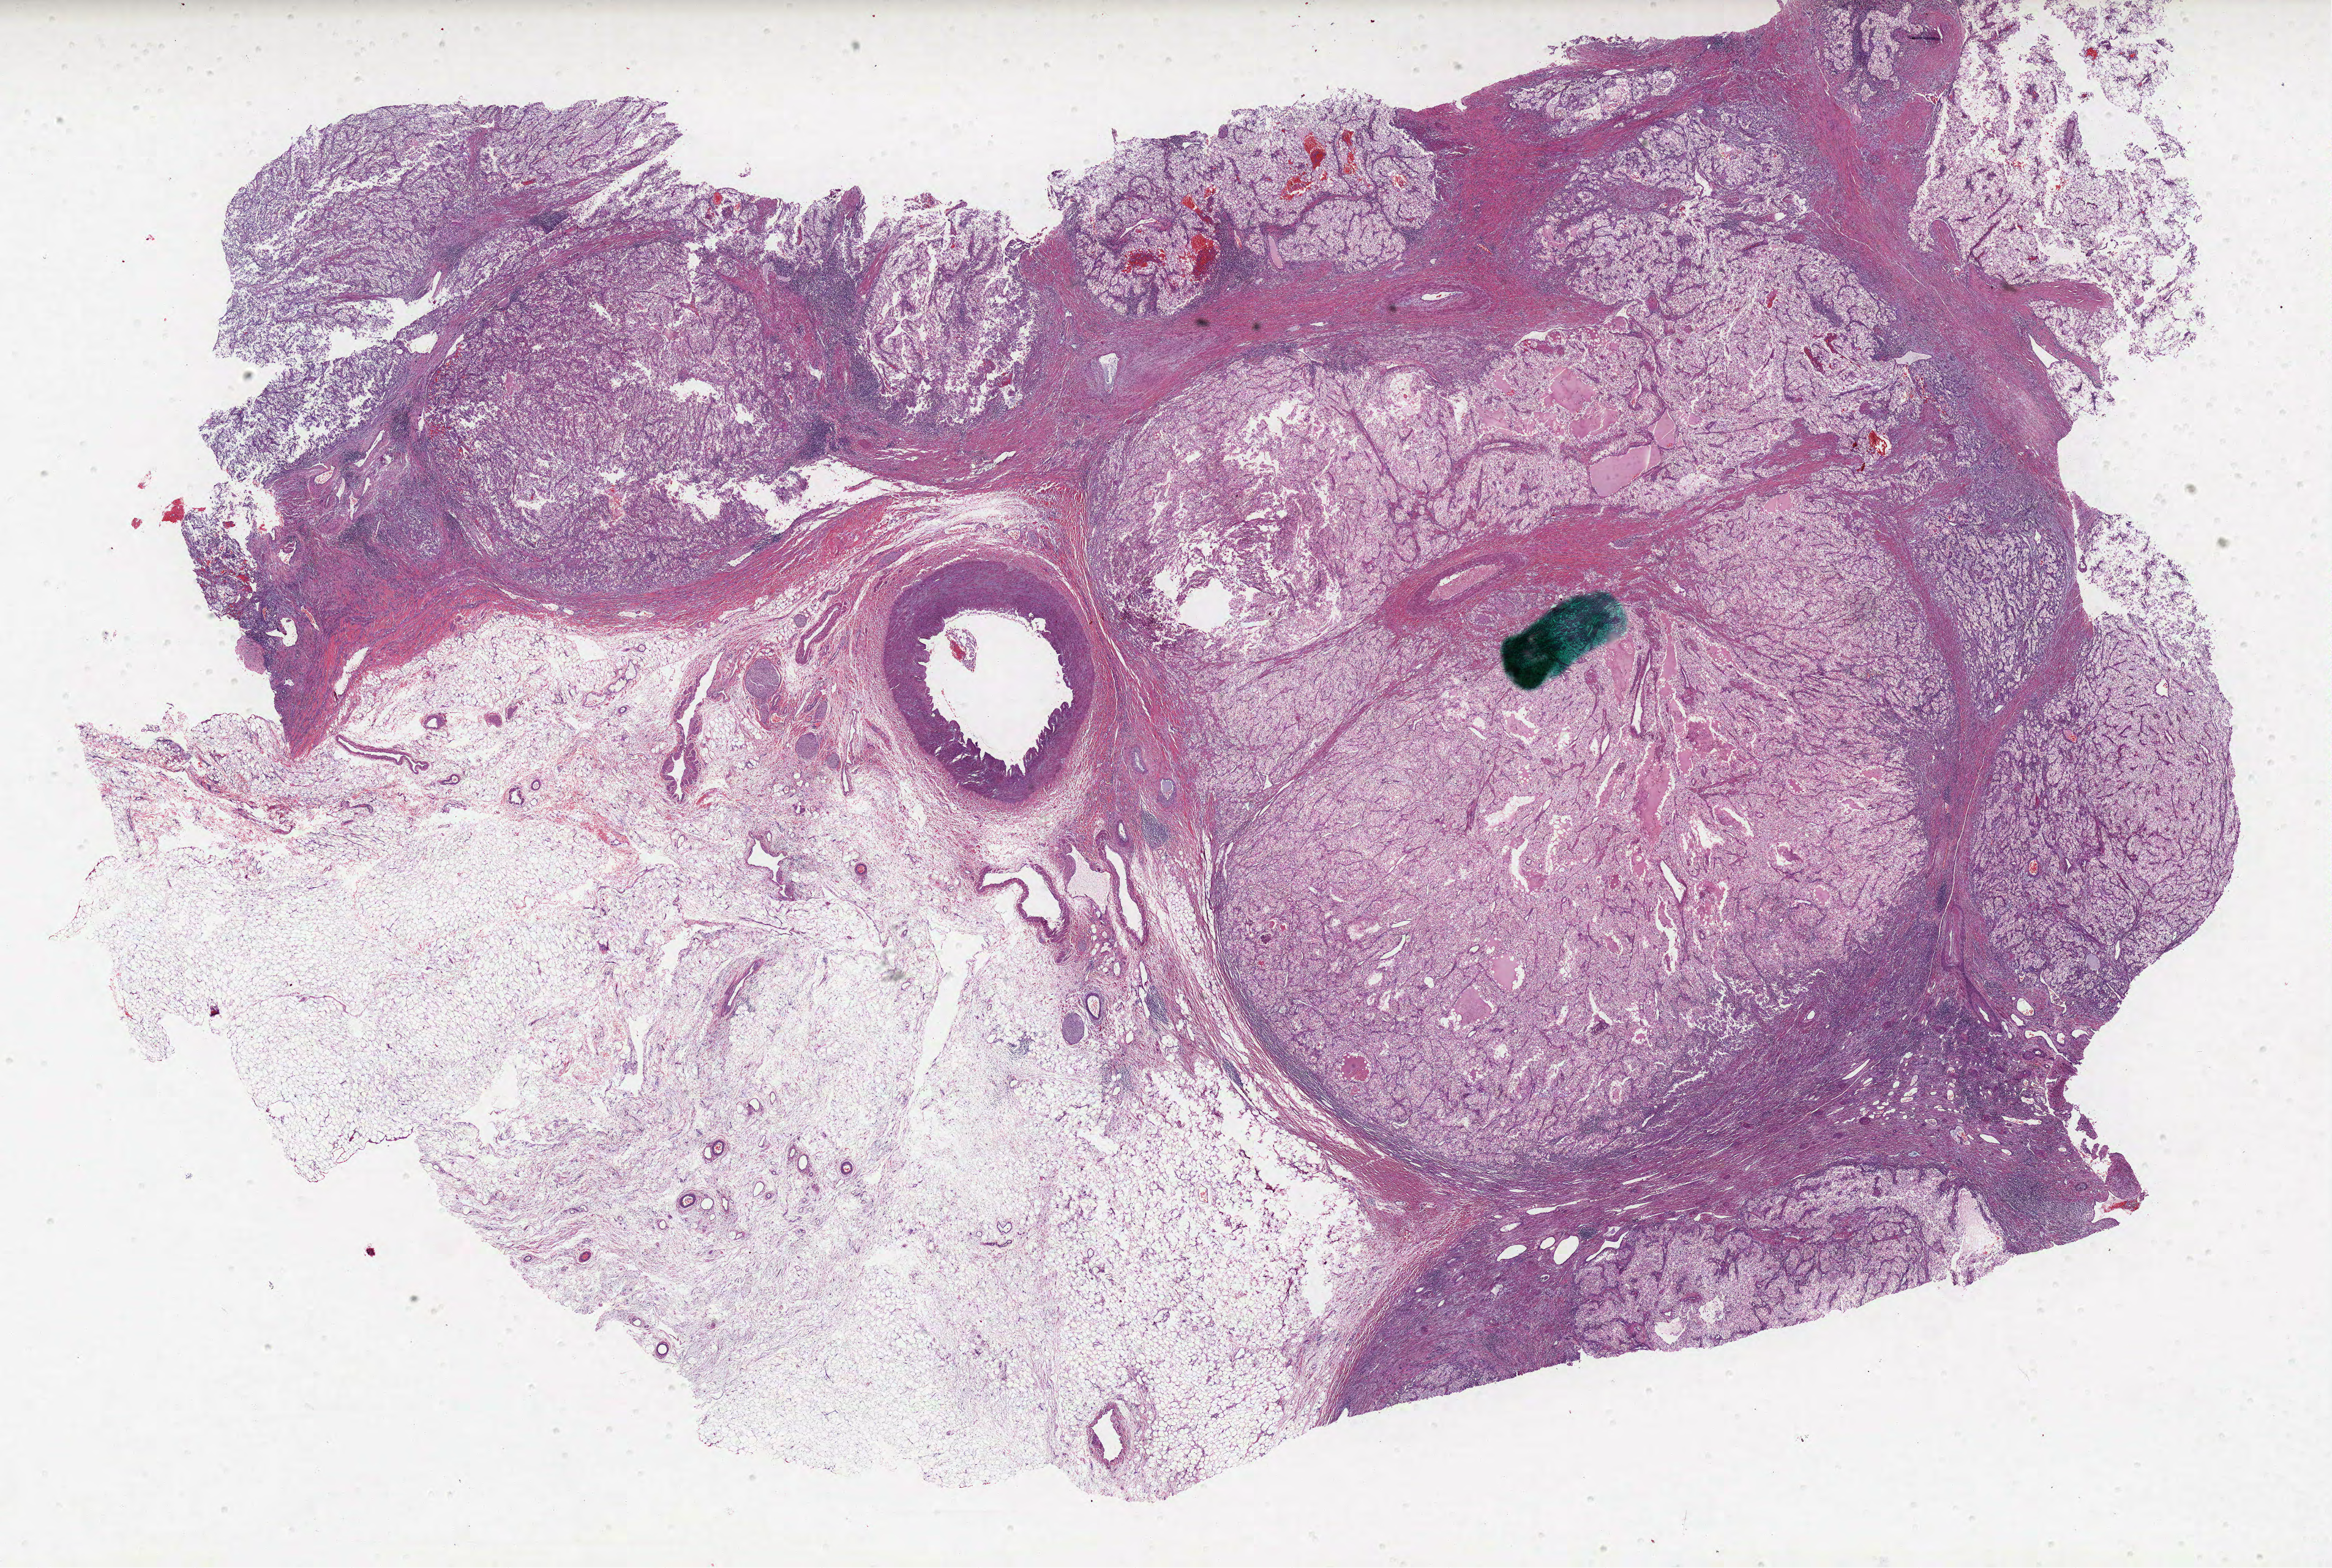
Digitized H&E-stained tissue section (whole slide) — low-resolution overview of the scanned area, about 30.4 x 20.5 mm; formalin-fixed paraffin-embedded (FFPE) diagnostic section; kidney, primary tumour sample. Male patient; age at initial diagnosis 58 years. Histologic grade: G4 (undifferentiated).
Pathologic diagnosis: Clear cell adenocarcinoma, NOS. Lymph nodes positive (case pathology): 0 of 7 examined. AJCC pathologic stage: IV.